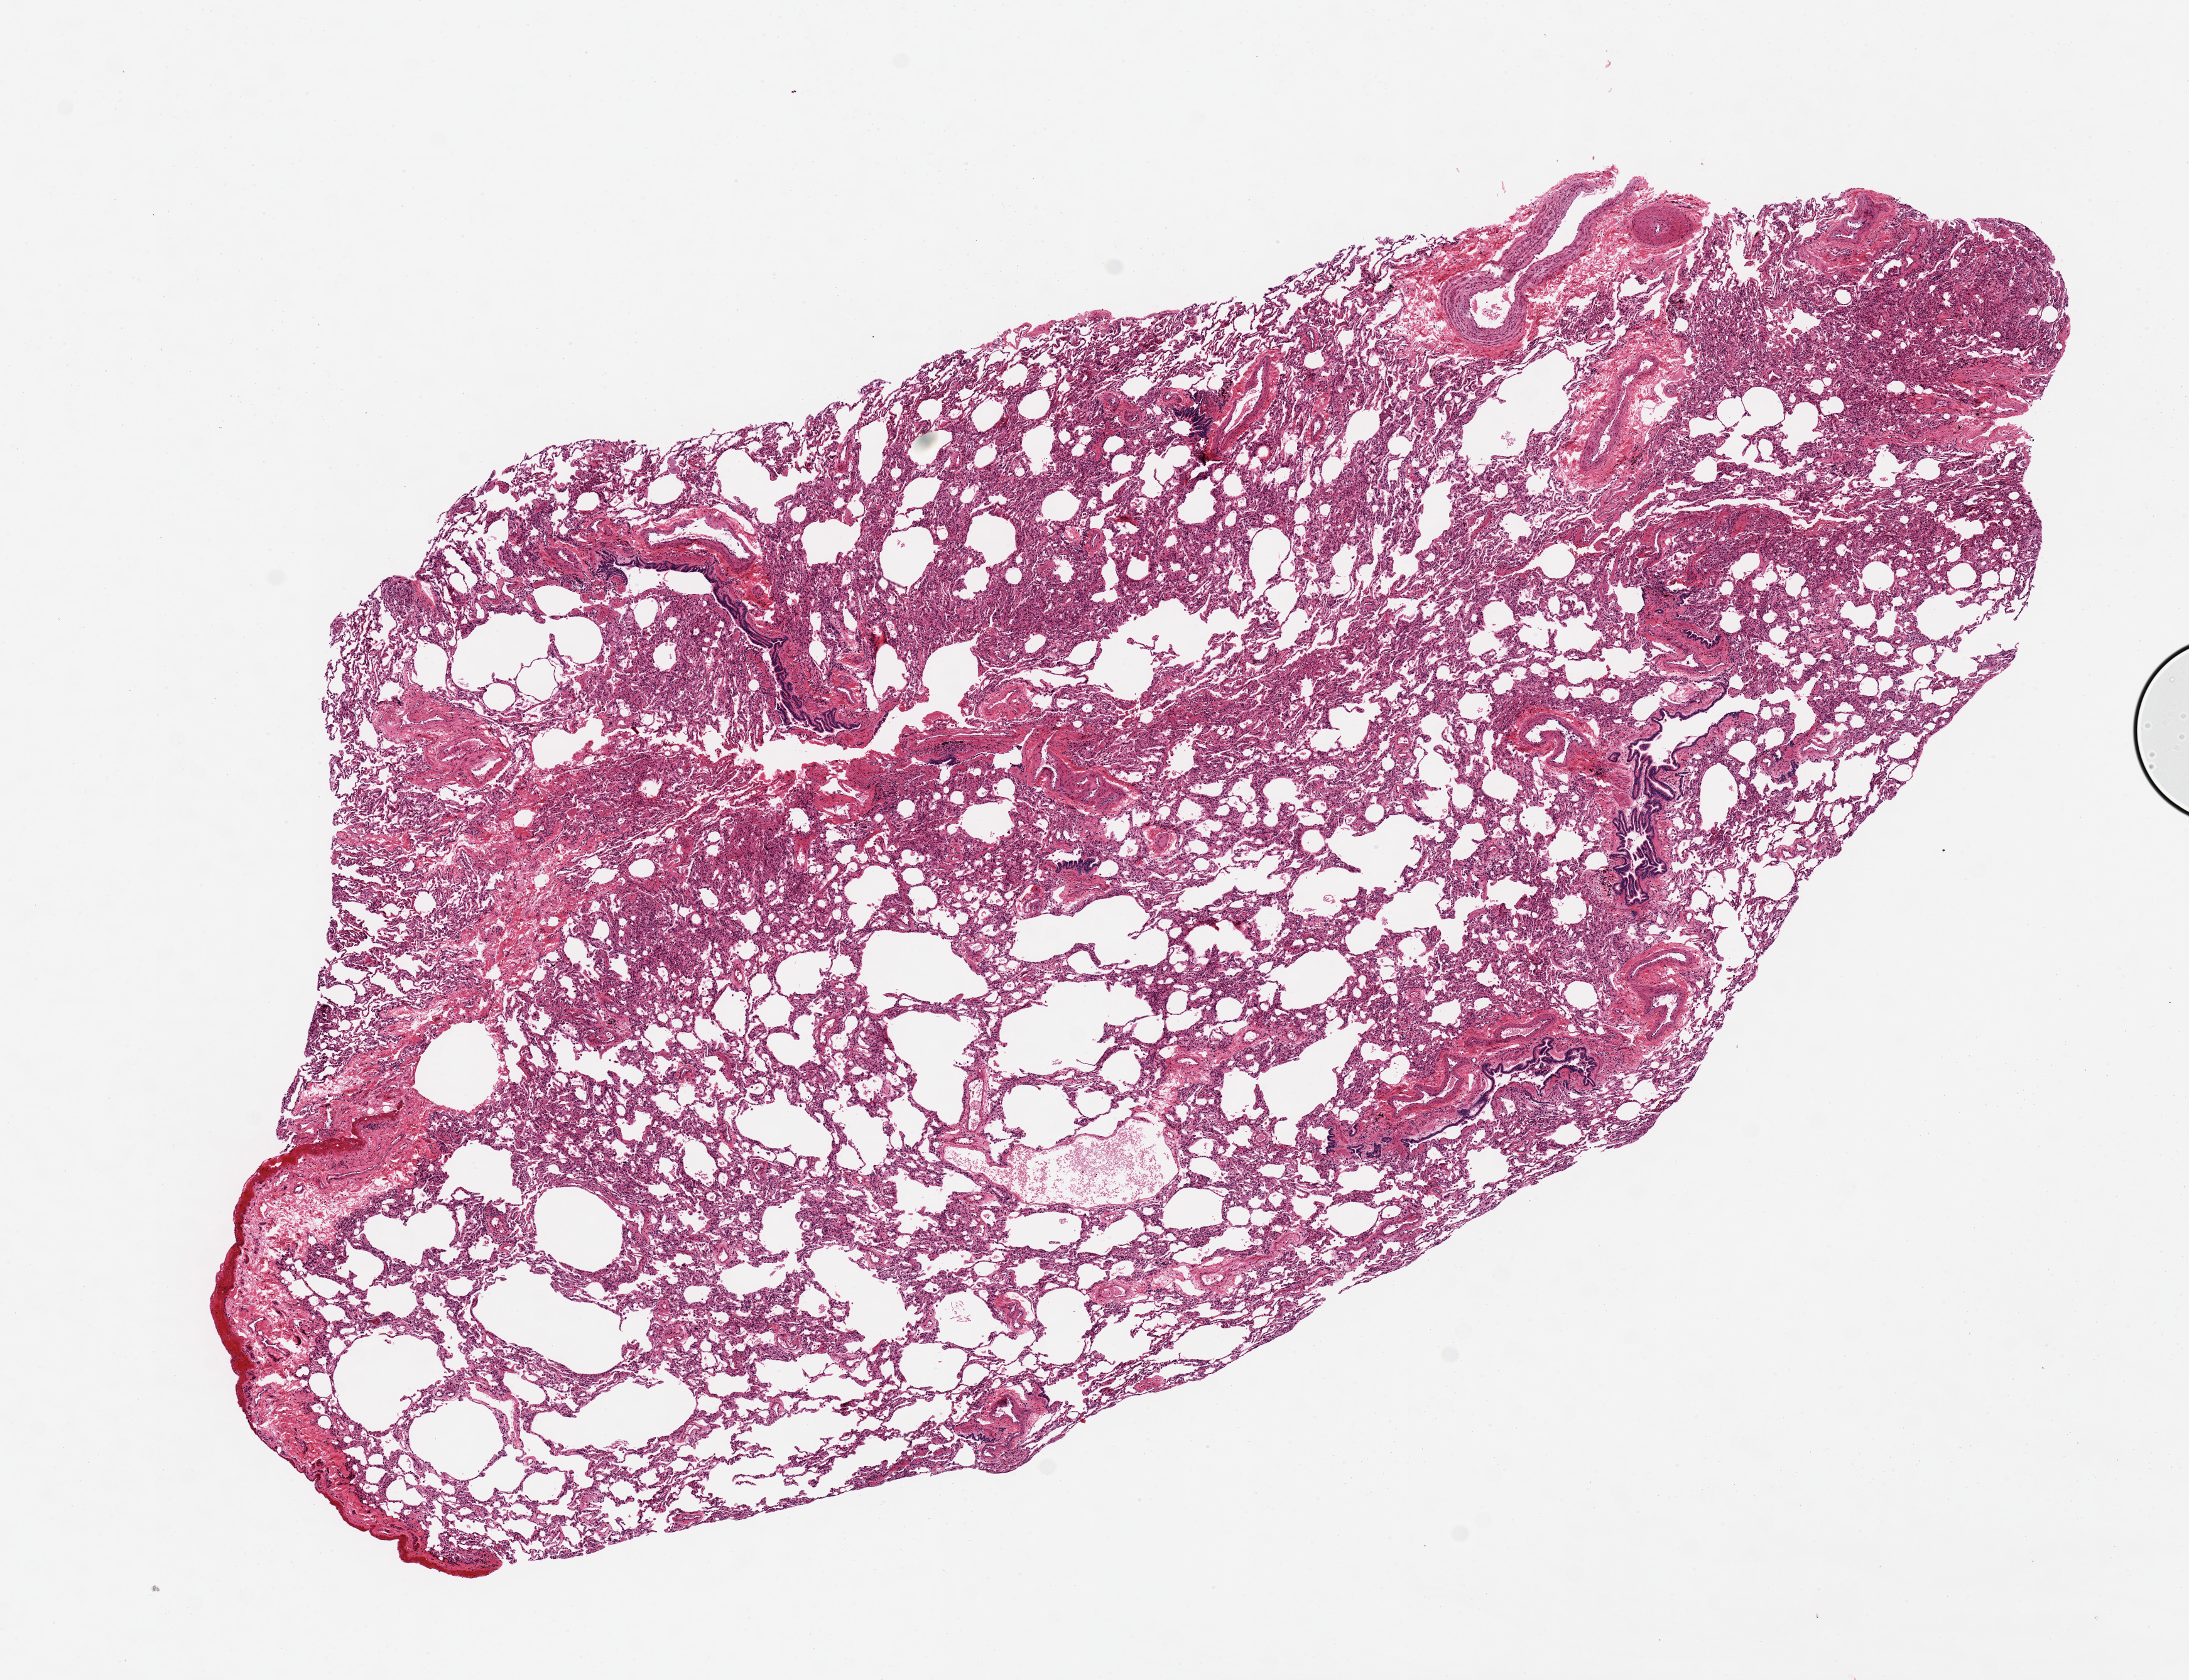
Whole-slide image, hematoxylin and eosin (H&E) stain, brightfield, shown as a low-resolution overview of the whole scanned area (about 13.8 x 10.6 mm, slide scanned at 20x). PAXgene-fixed paraffin-embedded (PFPE) section. Target tissue: lung. Donor tissue sample. Male donor.
Review note (as recorded): 1. 13.5x7mm. Patchy emphysematous changes, mild edema.